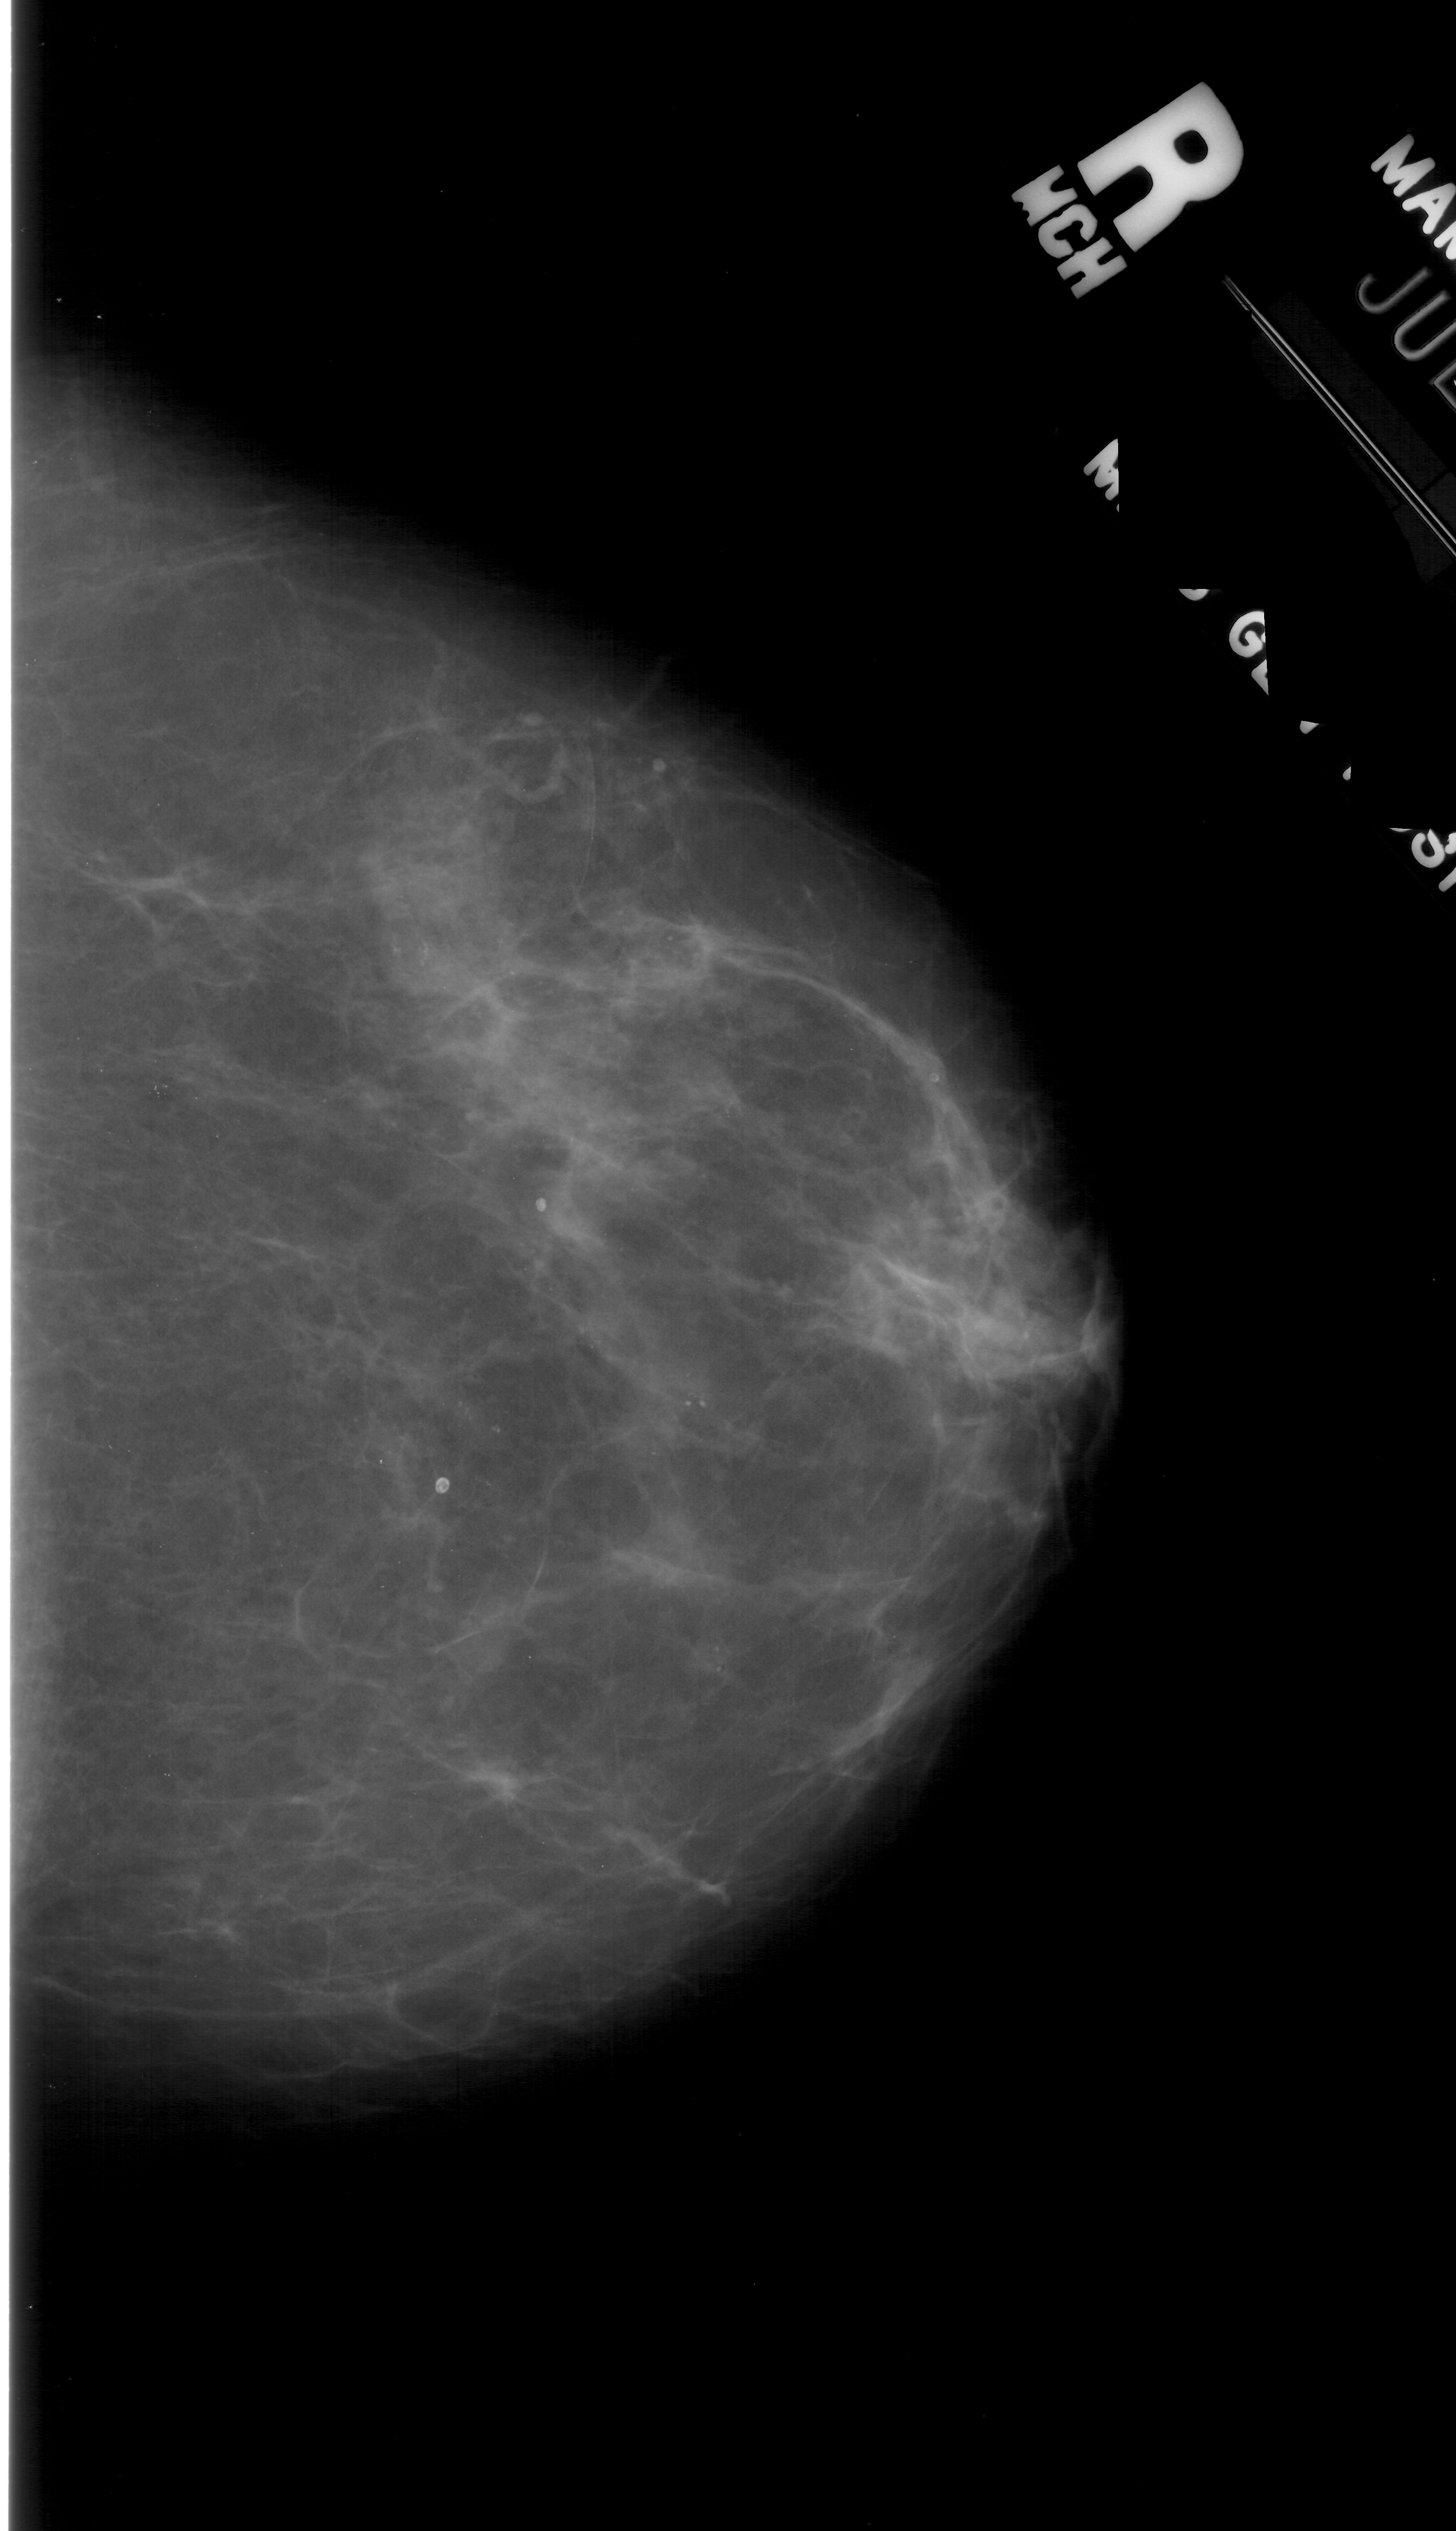
Mammogram (digitized film). Right breast. Craniocaudal (CC) view. BI-RADS breast density category 2 (scale 1–4). 1456 × 2531 image matrix.
Expert-marked regions of interest on this image (one box per marked abnormality):
- calcifications, morphology pleomorphic, distribution clustered; BI-RADS assessment category 4; pathology result (as recorded, not read from the image): benign: bounding box [x1, y1, x2, y2] px = [400, 925, 455, 977]